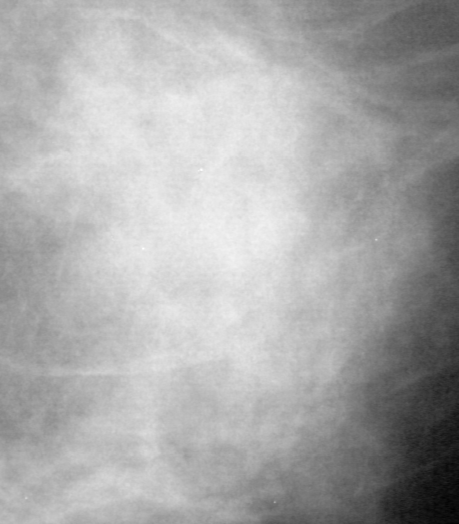
Cropped region of a digitized screen-film mammogram centred on a radiologist-marked abnormality; right breast; MLO view; BI-RADS breast density category 3 (scale 1–4).
- Mass, shape irregular, margins ill defined; BI-RADS assessment category 4; subtlety rating 4 on a 1 (subtle) to 5 (obvious) scale; pathology result (as recorded, not read from the image): benign.